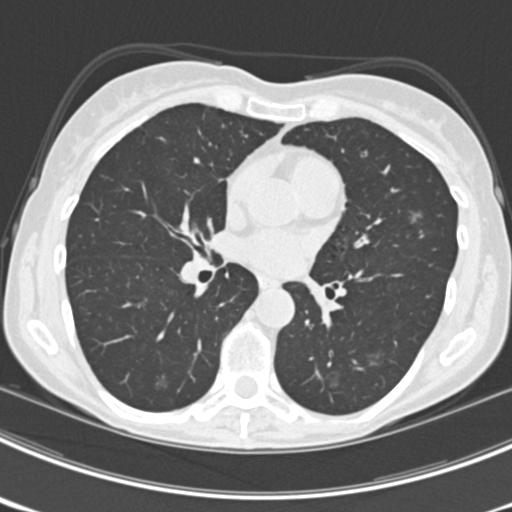
Axial slice from a low-dose chest CT screening exam; third annual screen; lung window (W 1500 / L -600 HU); standard (soft-tissue) reconstruction kernel (B30f); 512 × 512 image matrix, field of view 302 × 302 mm. Female, age 63 years at enrolment. Current smoker at enrolment.
- Expert reader's lesion annotation, bounding box <403,201,438,237> (left, top, right, bottom; pixels).
- The screening reader recorded 9 non-calcified nodules or masses ≥4 mm on this exam (left upper lobe, right upper lobe, left upper lobe, left lower lobe, right middle lobe, left lower lobe, left lower lobe, right lower lobe, right lower lobe); which of them this box marks is not recorded.
- Participant outcome: lung cancer diagnosed 15 days after this screen — bronchiolo-alveolar adenocarcinoma, NOS, right upper lobe, right middle lobe, right lower lobe, left upper lobe, left lower lobe, moderately differentiated (G2), stage IV (AJCC 6th edition).